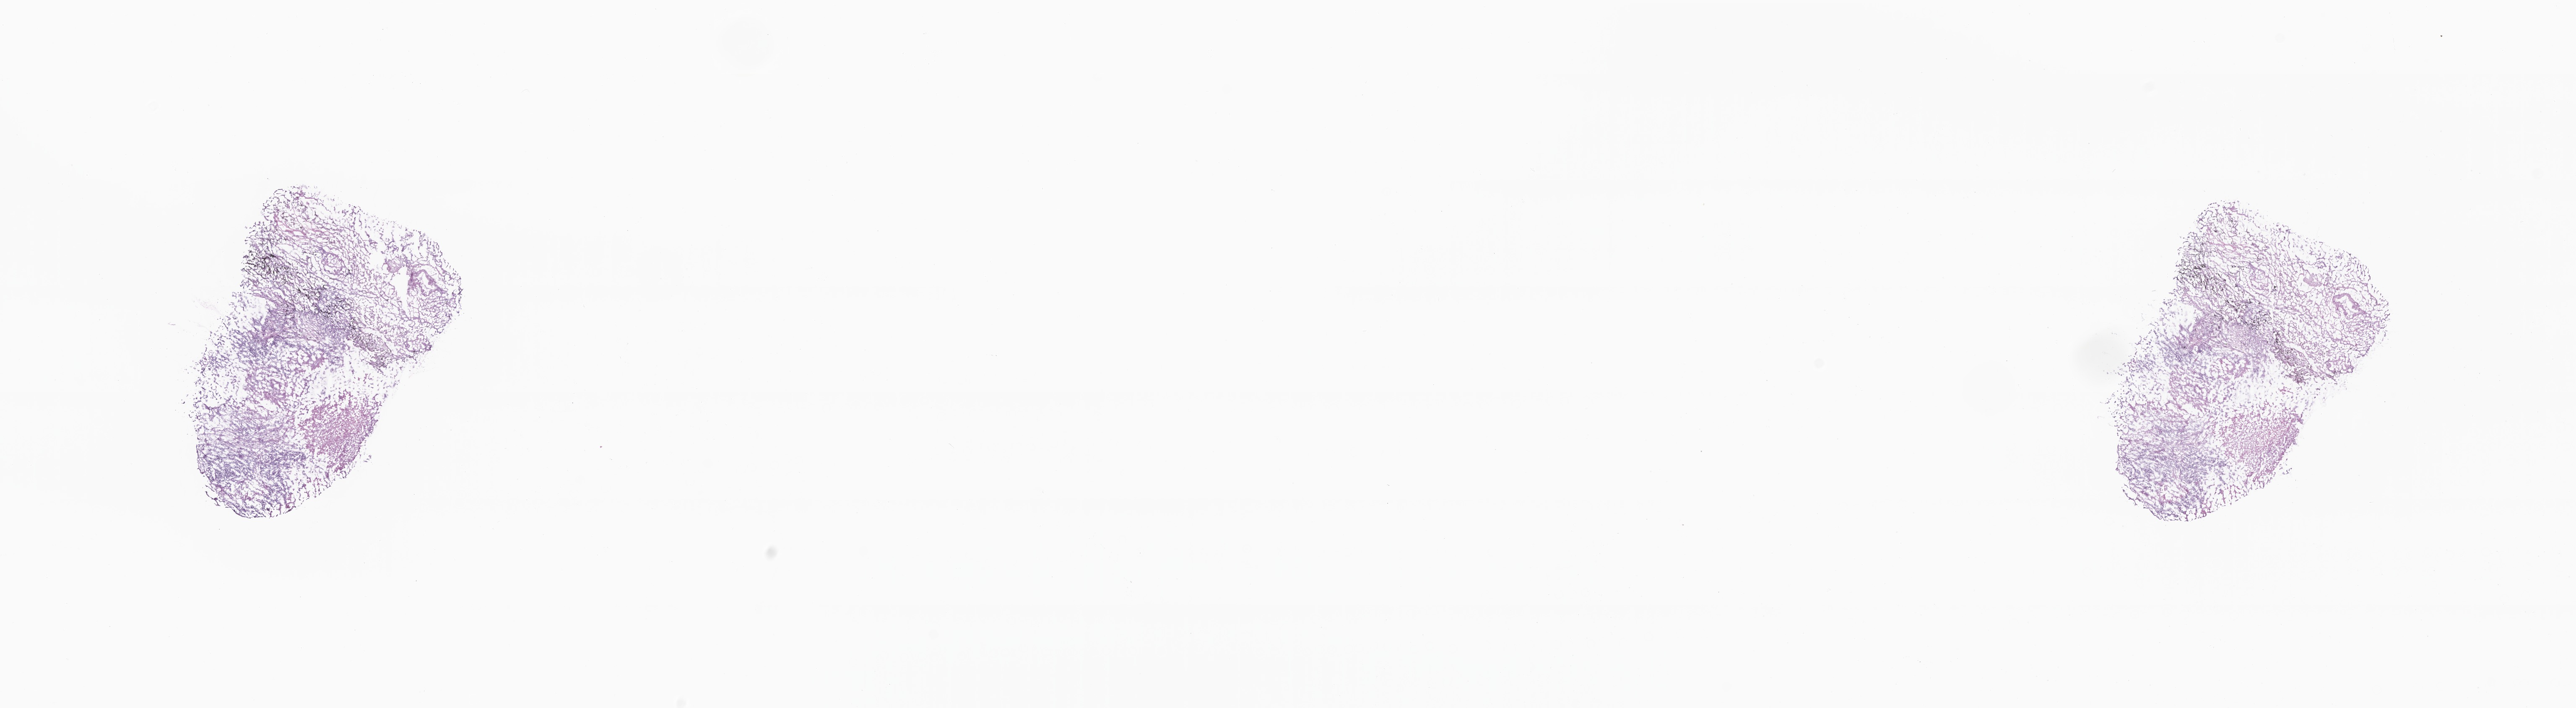
Haematoxylin and eosin whole-slide image — low-resolution overview of the scanned area, about 25.9 x 7.1 mm, frozen section (tissue freezing medium), primary tumor, site: upper lobe of left lung. Female patient; age at initial diagnosis 83 years. Composition of this section per pathologist review: tumor cells 30%, tumor nuclei 40%, stromal cells 0%, necrosis 20%, normal cells 50%. Inflammatory infiltration, as recorded: lymphocyte infiltration 0%, monocyte infiltration 0%, neutrophil infiltration 0%.
• diagnosis: Squamous cell carcinoma, NOS